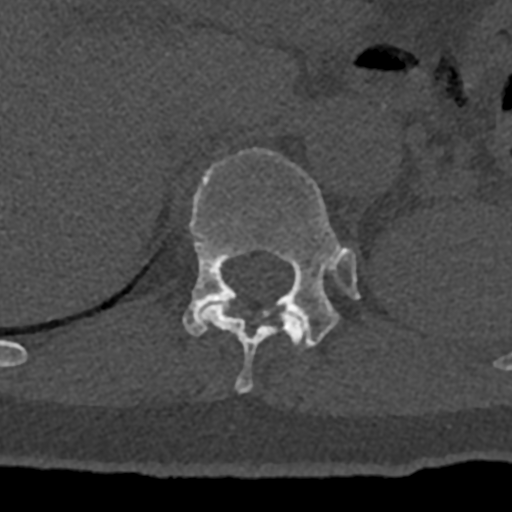
CT including the spine, one axial slice. Position 513 of 797 along the scan axis. Reconstruction kernel Br40s/3. Bone window (W 1800 / L 400 HU). 0.5 mm slice thickness. 512 × 512 image matrix, field of view 160 × 160 mm. Male patient, age 74 years. Case-level facts recorded for this patient, not image findings: primary cancer: renal; vertebrae with lytic lesions (as recorded): T10, L1, L2, L3, L4, L5.
Outlined on this slice (semi-automatically segmented with operator editing):
- T11 vertebra: box from (x=200, y=301) to (x=304, y=393) px
- T12 vertebra: (x=182, y=148)–(x=360, y=347)